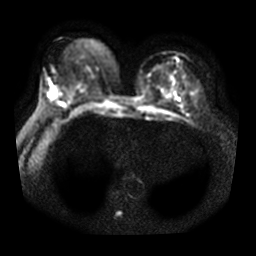
Breast MRI, one axial slice. Diffusion-weighted series; image 2 of 4 stored at this slice position (different b-values; order by instance number). 3 T. 256 × 256 image matrix, field of view 340 × 340 mm. Female patient.
Annotated regions visible in this slice (manually delineated by an expert):
- tumour on diffusion-weighted imaging: bounding box <48,82,56,99> (left, top, right, bottom; pixels)